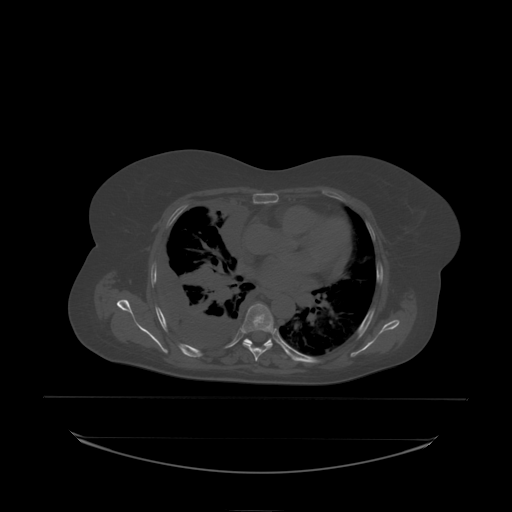
CT including the spine, one axial slice; slice 147 of 242 in the series (ordered by position); bone window (W 1800 / L 400 HU); 512 × 512 image matrix, field of view 500 × 500 mm. Patient: female, 53 years. From the clinical record (not read from this slice): primary cancer: lung; vertebrae with lytic lesions (as recorded): T7, L1.
Structures marked on this image (semi-automatically segmented with operator editing):
- T6 vertebra: bounding box <242,304,274,334> (left, top, right, bottom; pixels)